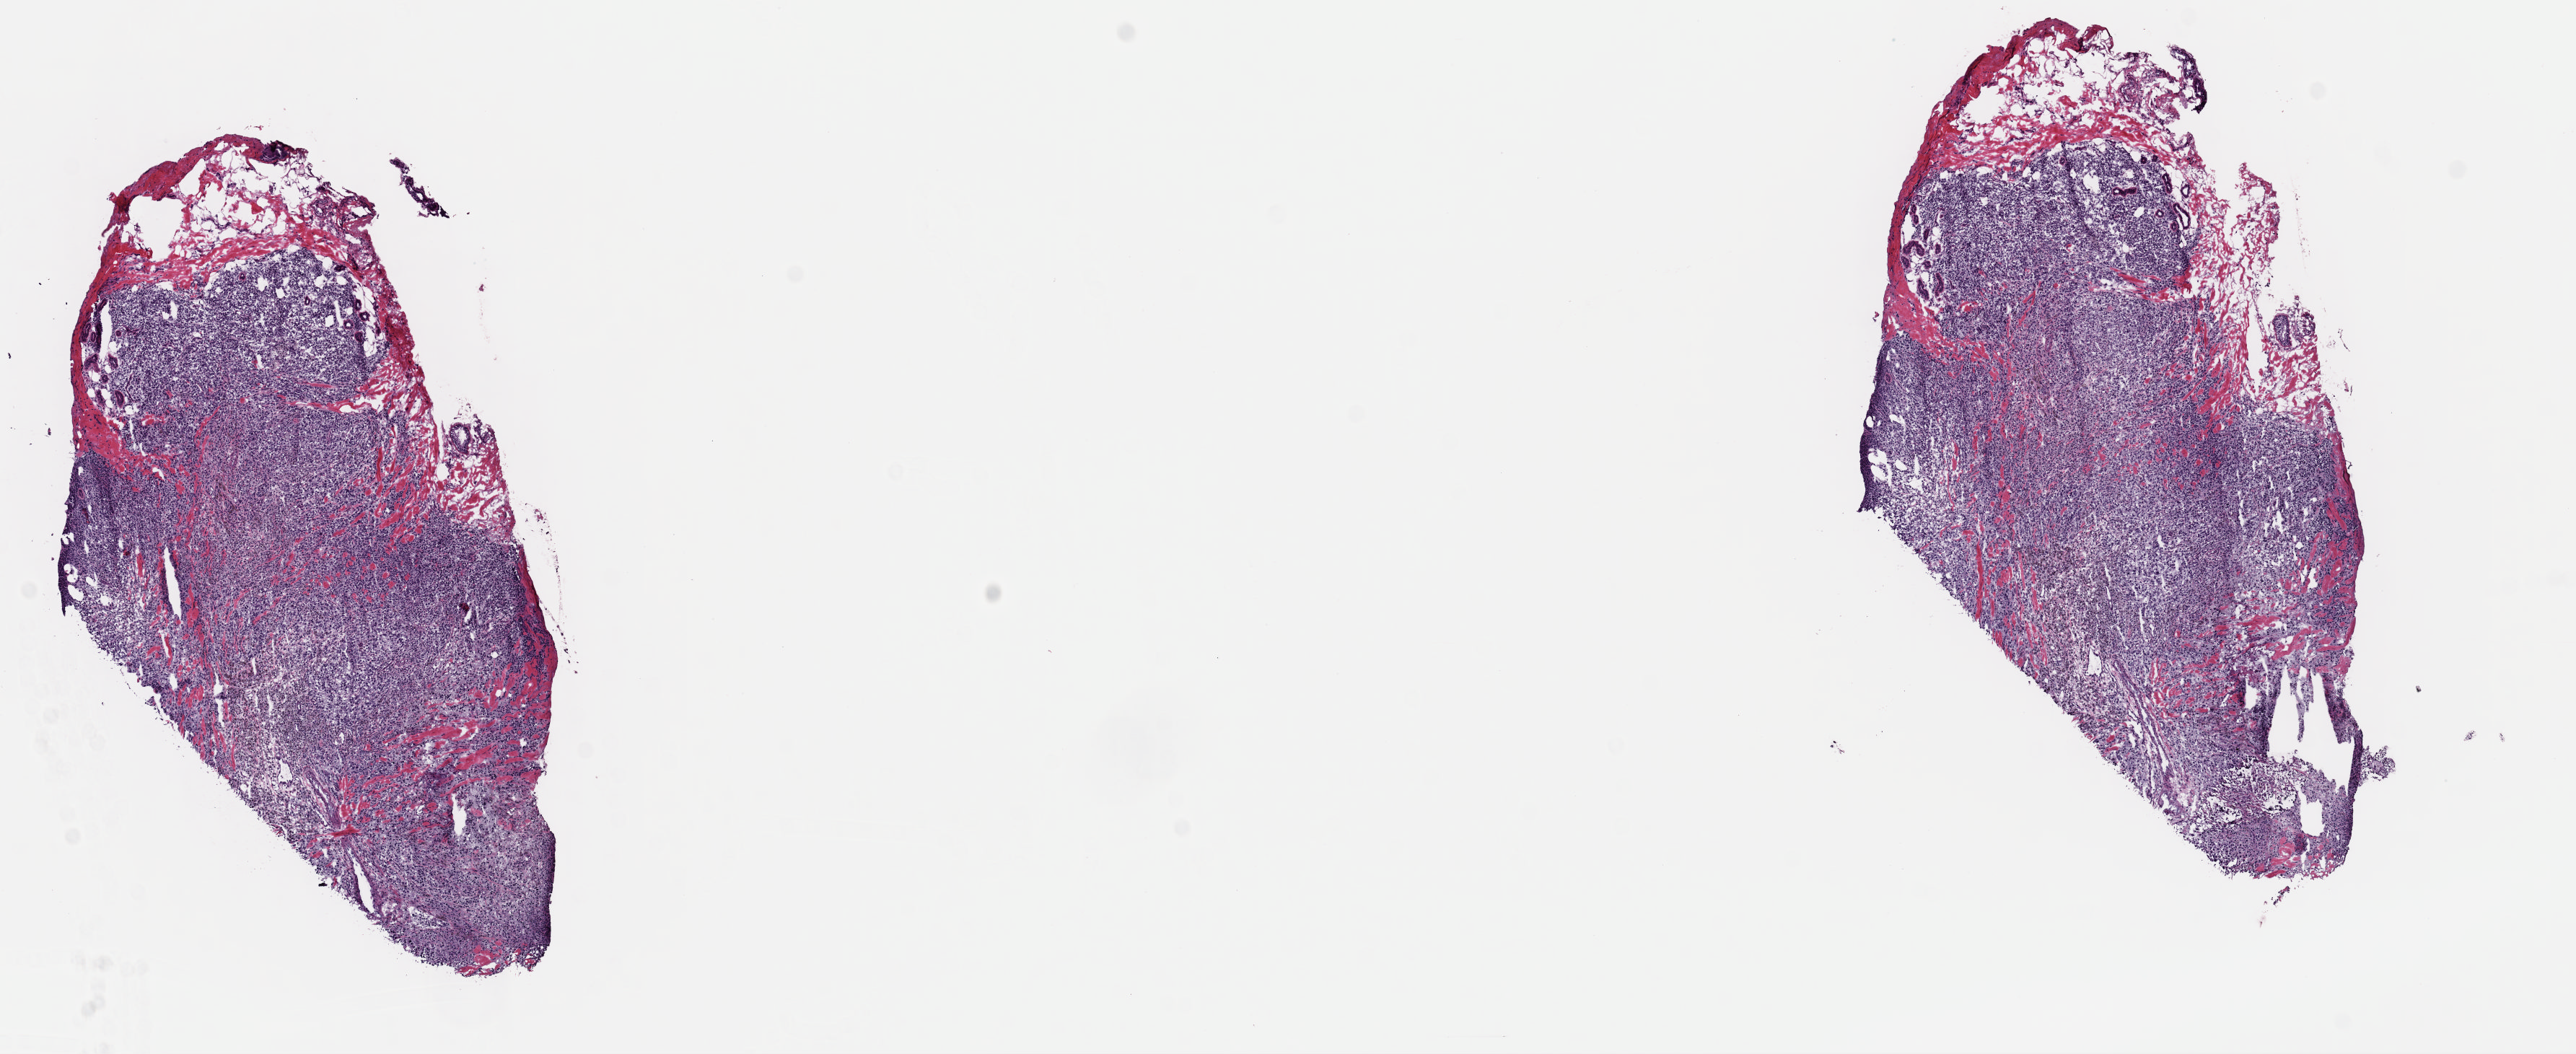
Hematoxylin and eosin (H&E) stained whole-slide image — shown as a low-resolution overview of the whole scanned area (about 14.1 x 5.8 mm, slide scanned at 40x), frozen section from the top of the tissue portion, metastatic tumour sample, sampled site: lymph node. Male, age 57 years at initial diagnosis.
This section: metastatic tumour tissue. Patient diagnosis: Malignant melanoma, NOS.